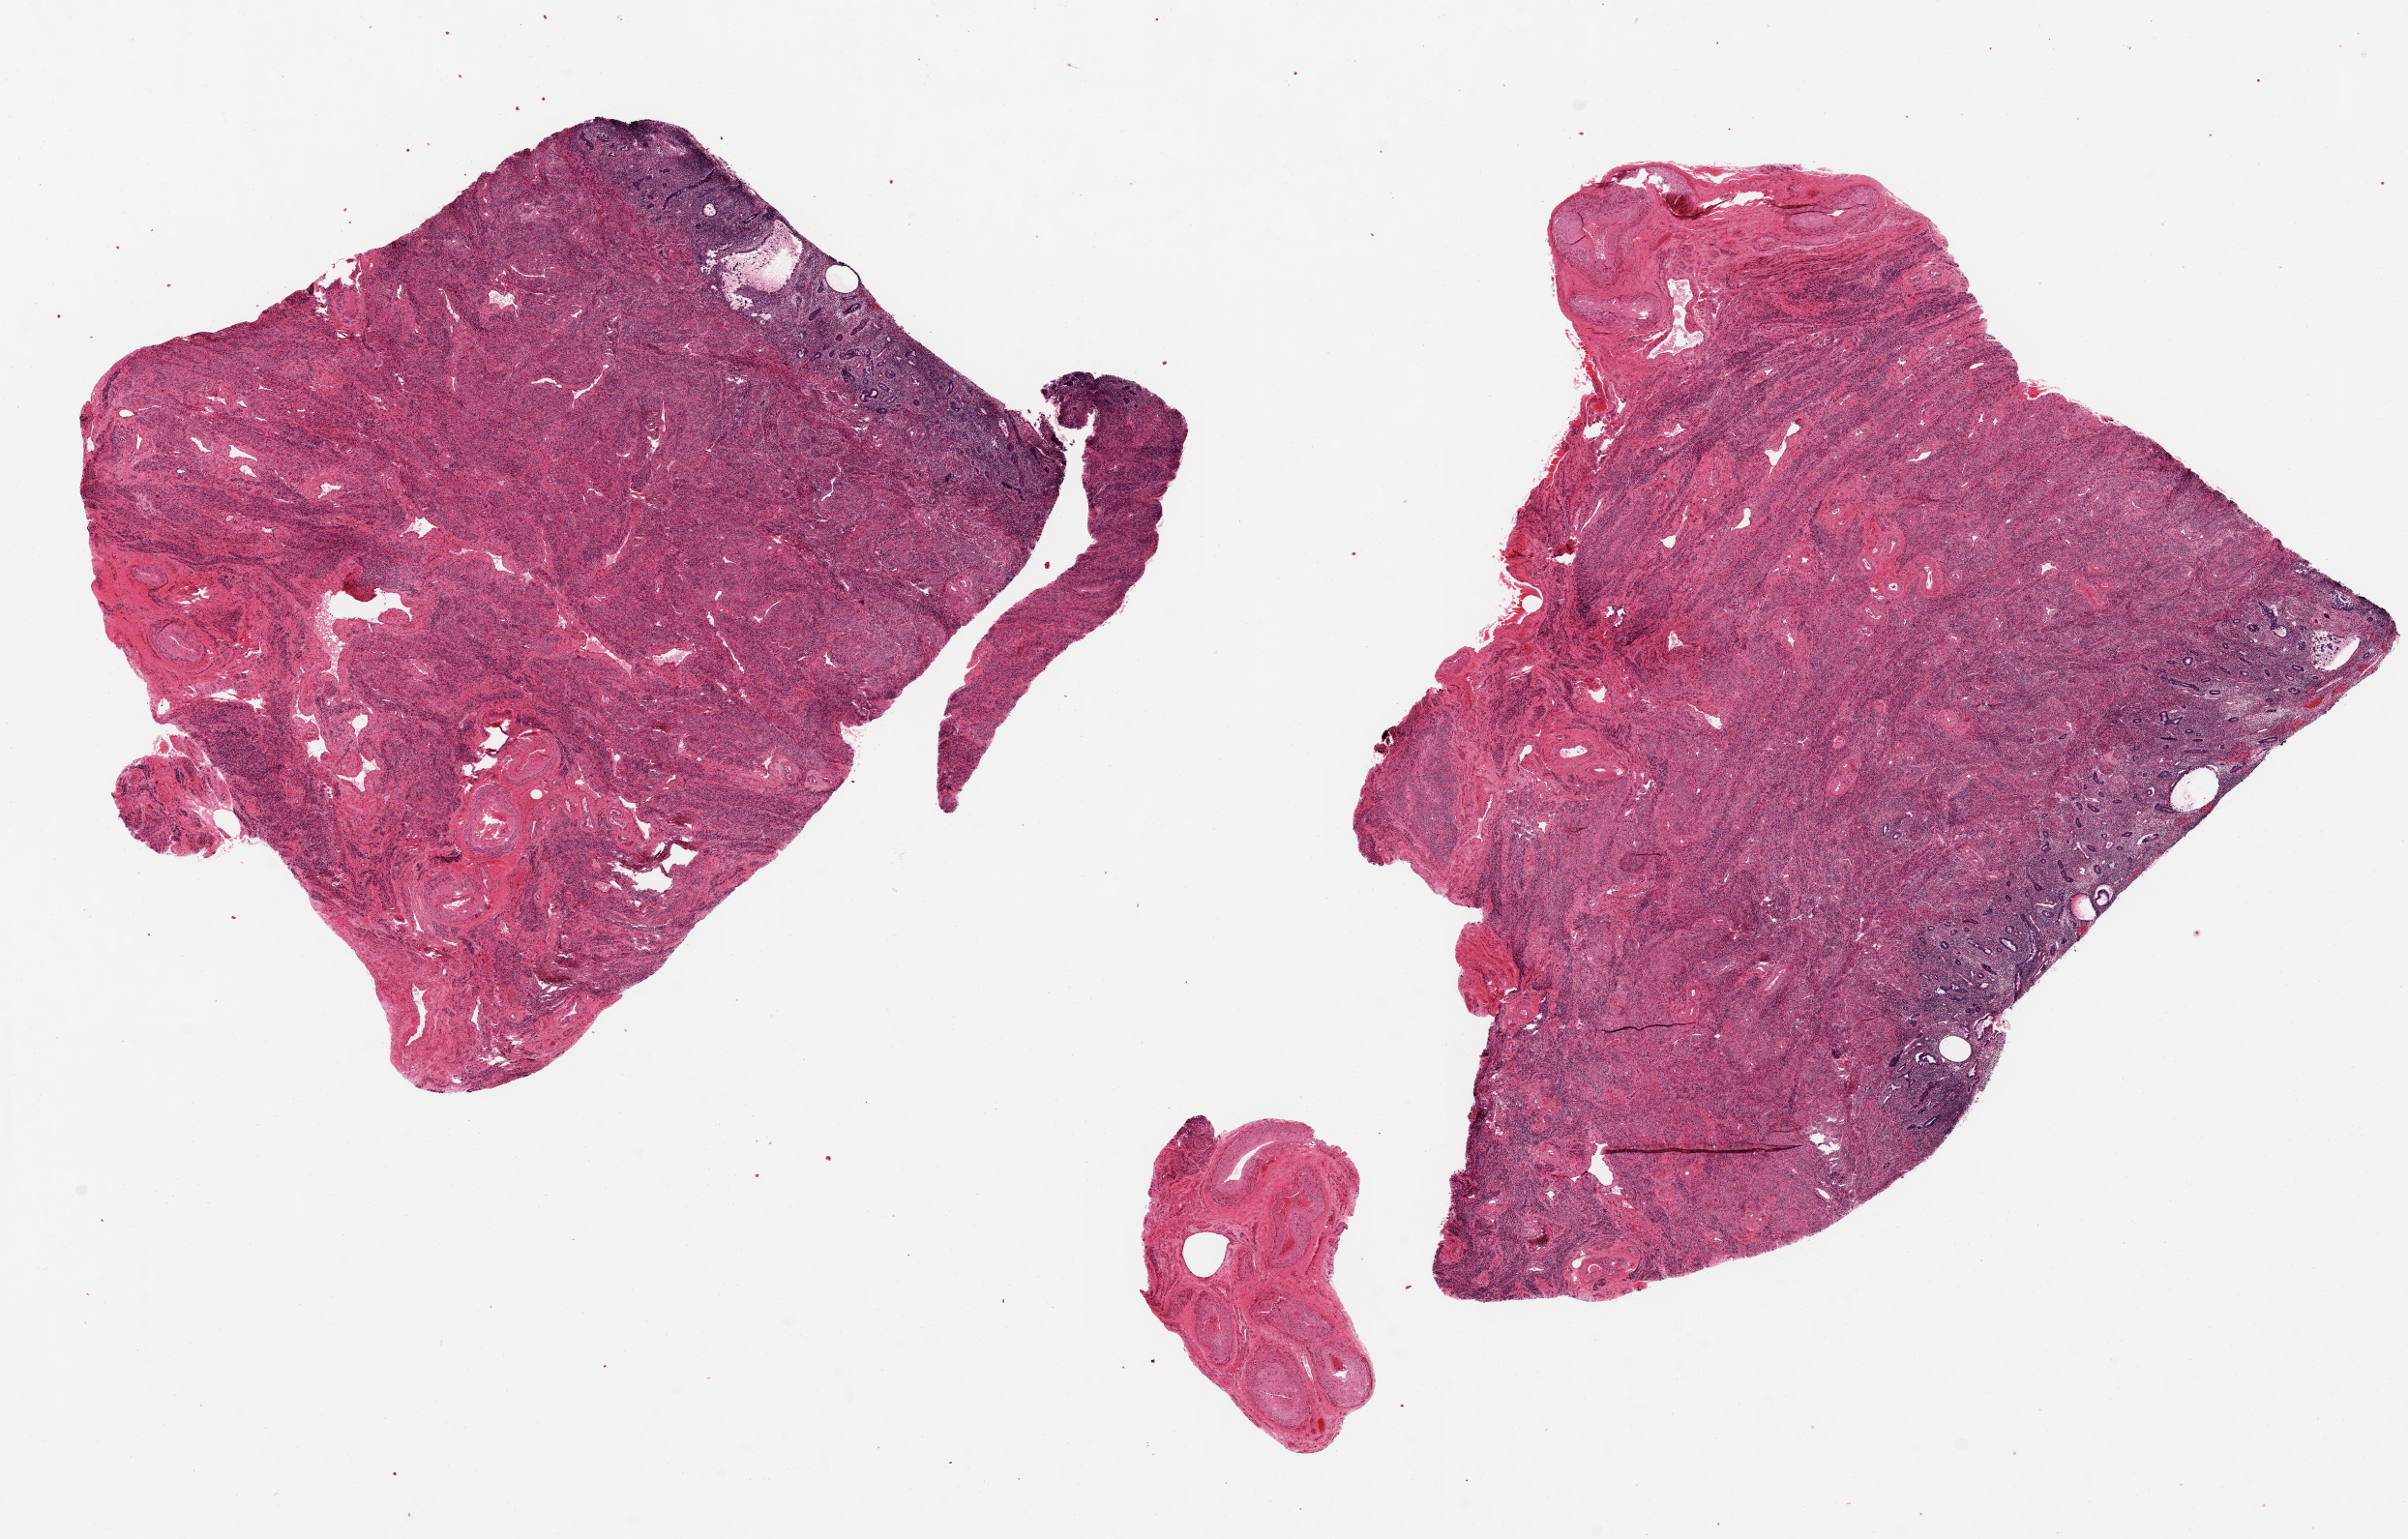
Whole-slide image, haematoxylin and eosin stain, low-resolution overview of the scanned area, about 19.7 x 12.6 mm (slide scanned at 20x). PAXgene-fixed, paraffin-embedded tissue. Sampled site (target tissue): uterus. Tissue donor sample. Donor: female.
Review note (as recorded): 2 aliquots, ~6x6mm. Endometrial glands/stroma are ~10% of thickness, glands poorly preserved.